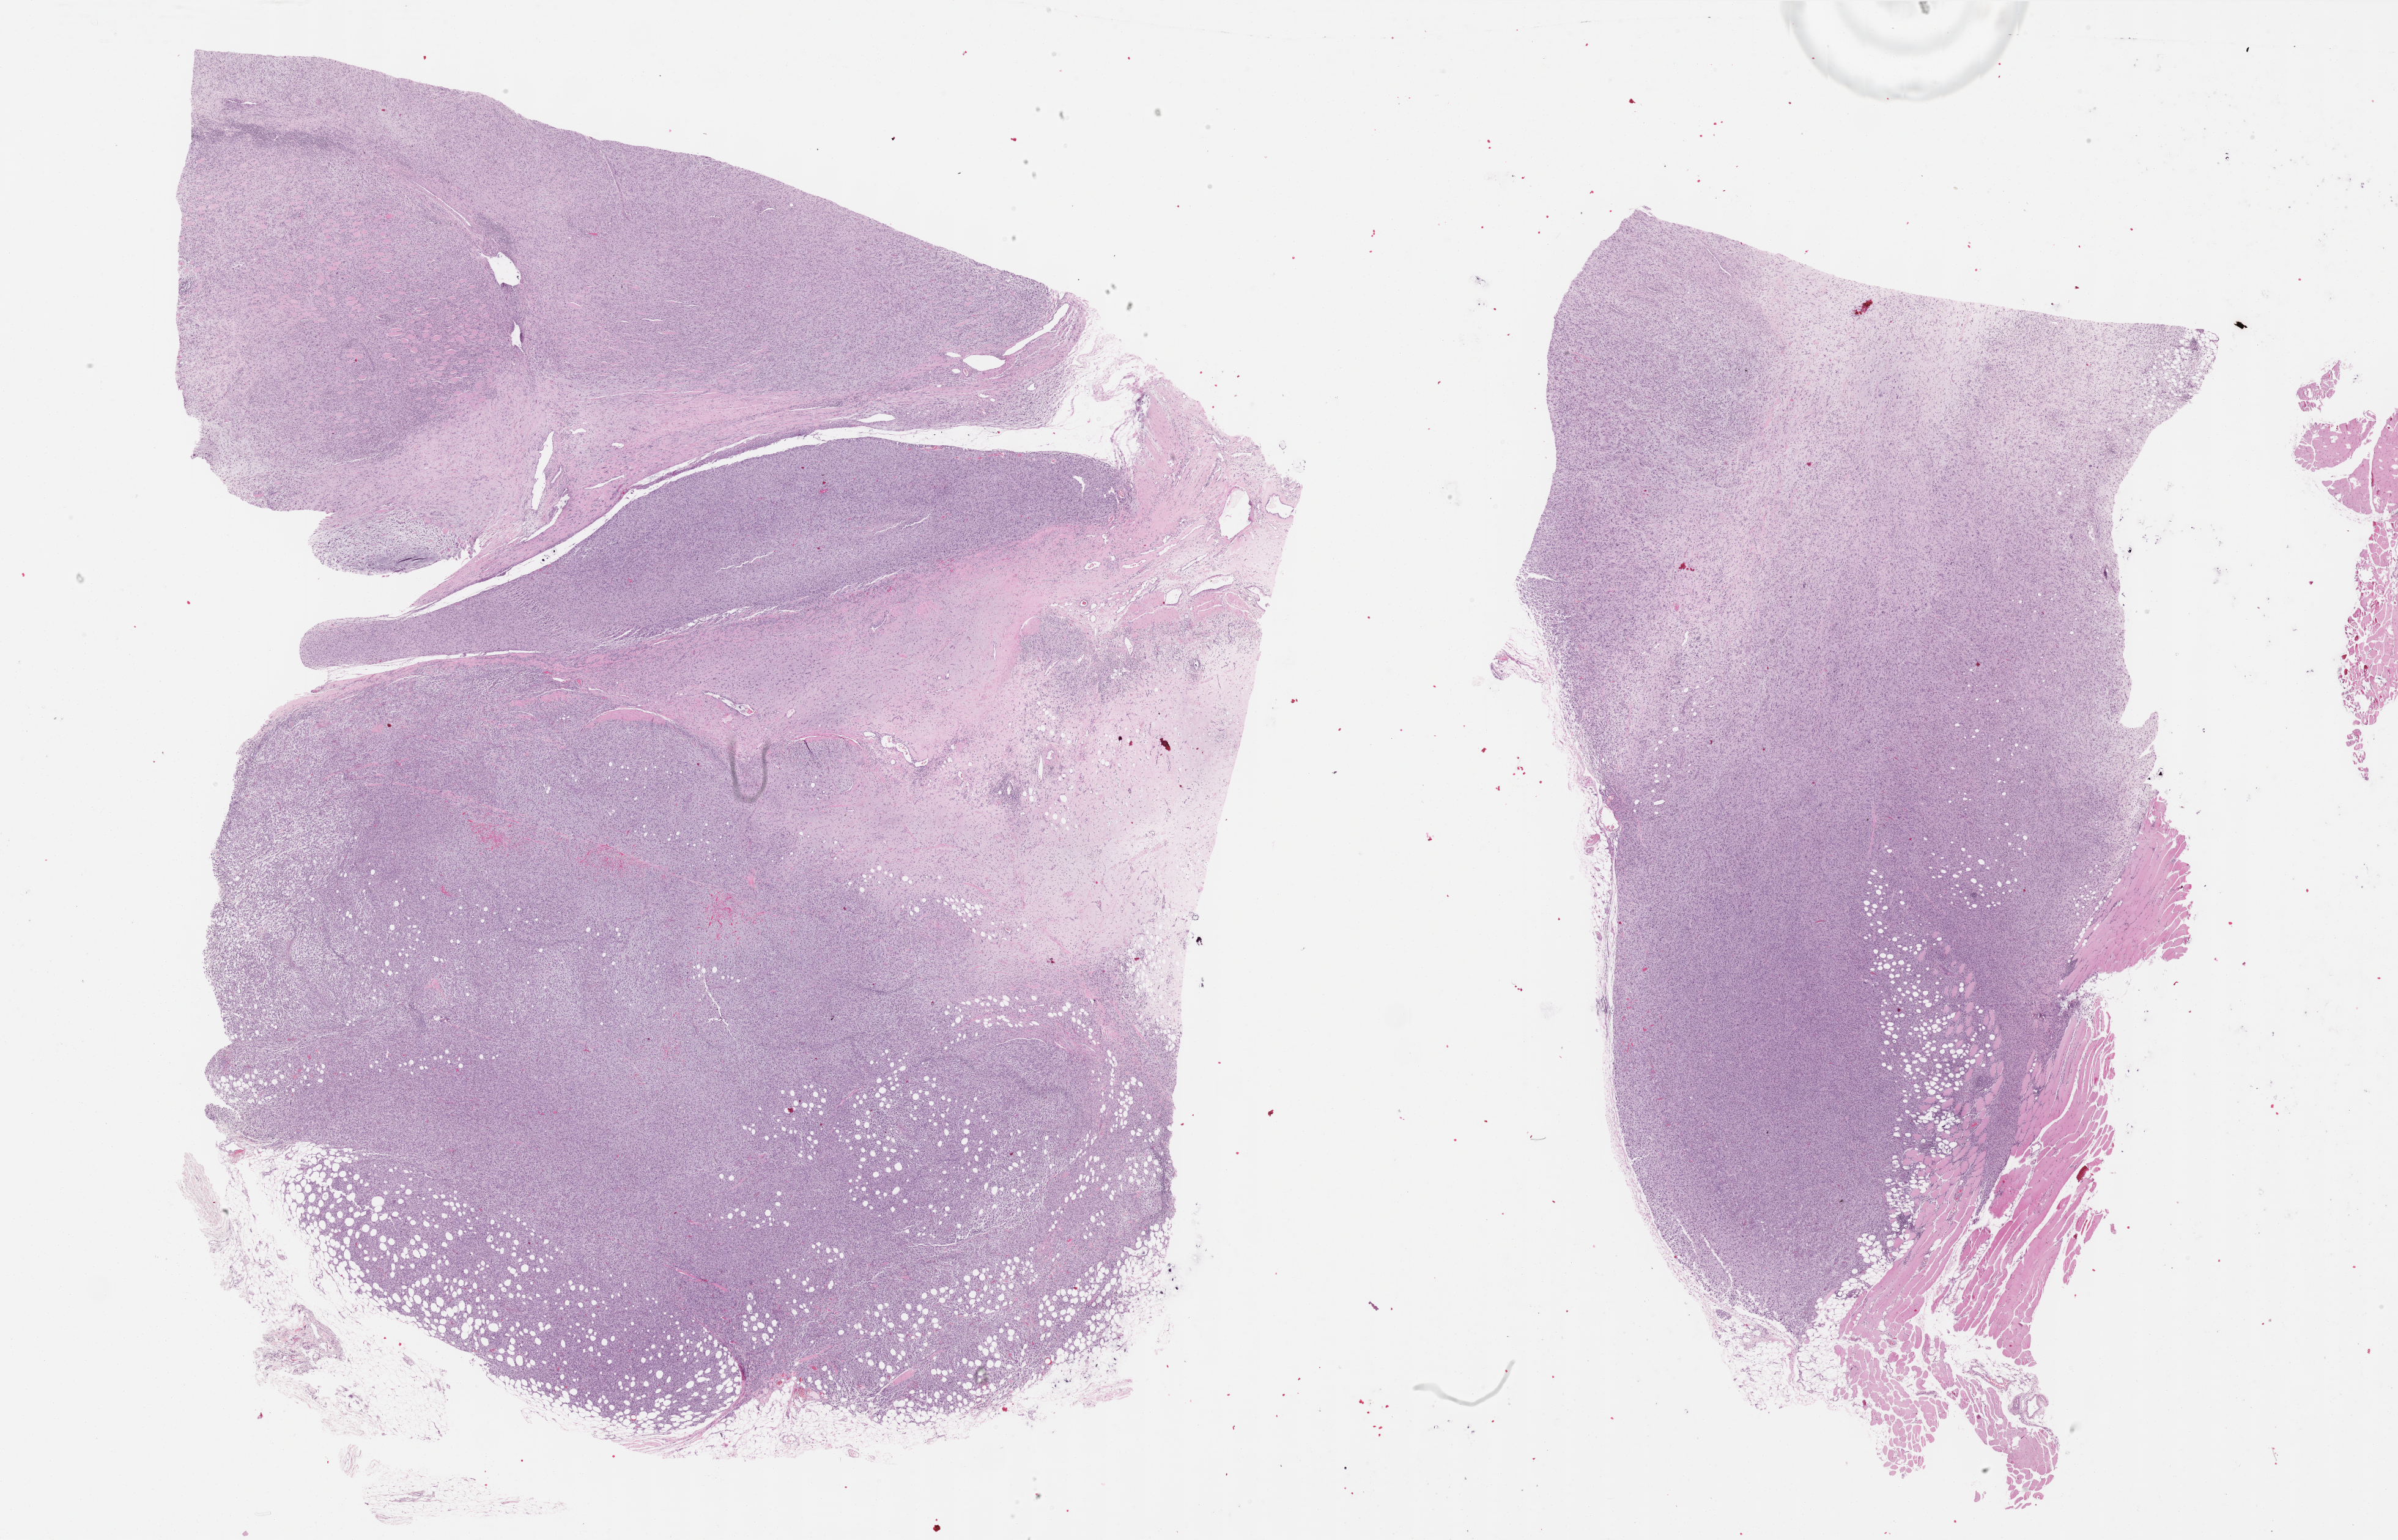
Whole-slide histology image, H&E — shown as a low-resolution overview of the whole scanned area (about 31.7 x 20.4 mm), formalin-fixed paraffin-embedded (FFPE) diagnostic section, primary tumour sample from the connective, subcutaneous and other soft tissues. Female patient; age at initial diagnosis 86 years.
Histologic diagnosis: Fibromyxosarcoma (connective, subcutaneous and other soft tissues of pelvis).